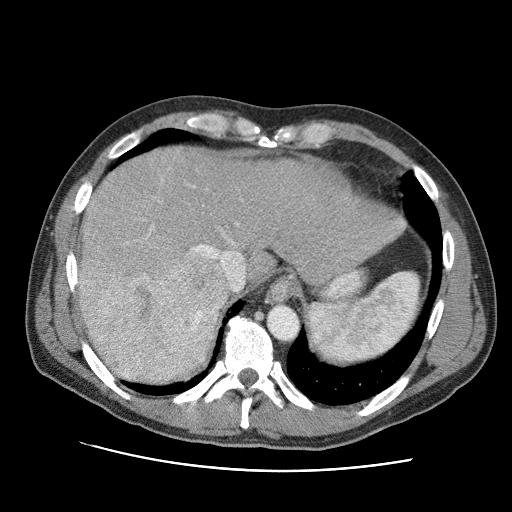
Contrast-enhanced abdominal CT (liver protocol), one axial slice; position 77 of 95 along the scan axis; reconstruction kernel STANDARD; one of 2 acquisitions stored at this slice position; soft-tissue window (W 400 / L 40 HU); 2.5 mm slice thickness; 512 × 512 image matrix. From the clinical record (not read from this slice): diagnosis: hepatocellular carcinoma (patient treated with transarterial chemoembolisation; whether this scan precedes or follows treatment is not stated here); TNM stage (as recorded): Stage-IVA; Child-Pugh class: A; tumour differentiation: moderately differentiated; tumour nodularity: multinodular.
Annotated regions visible in this slice (semi-automatically segmented with operator editing):
- liver parenchyma outside the tumour (the mass and vessels are separate outlines, so this box may not span the whole liver): bounding box <78,146,406,382> (left, top, right, bottom; pixels)
- mass: <78,254,227,382>
- liver vessels: <89,186,246,303>